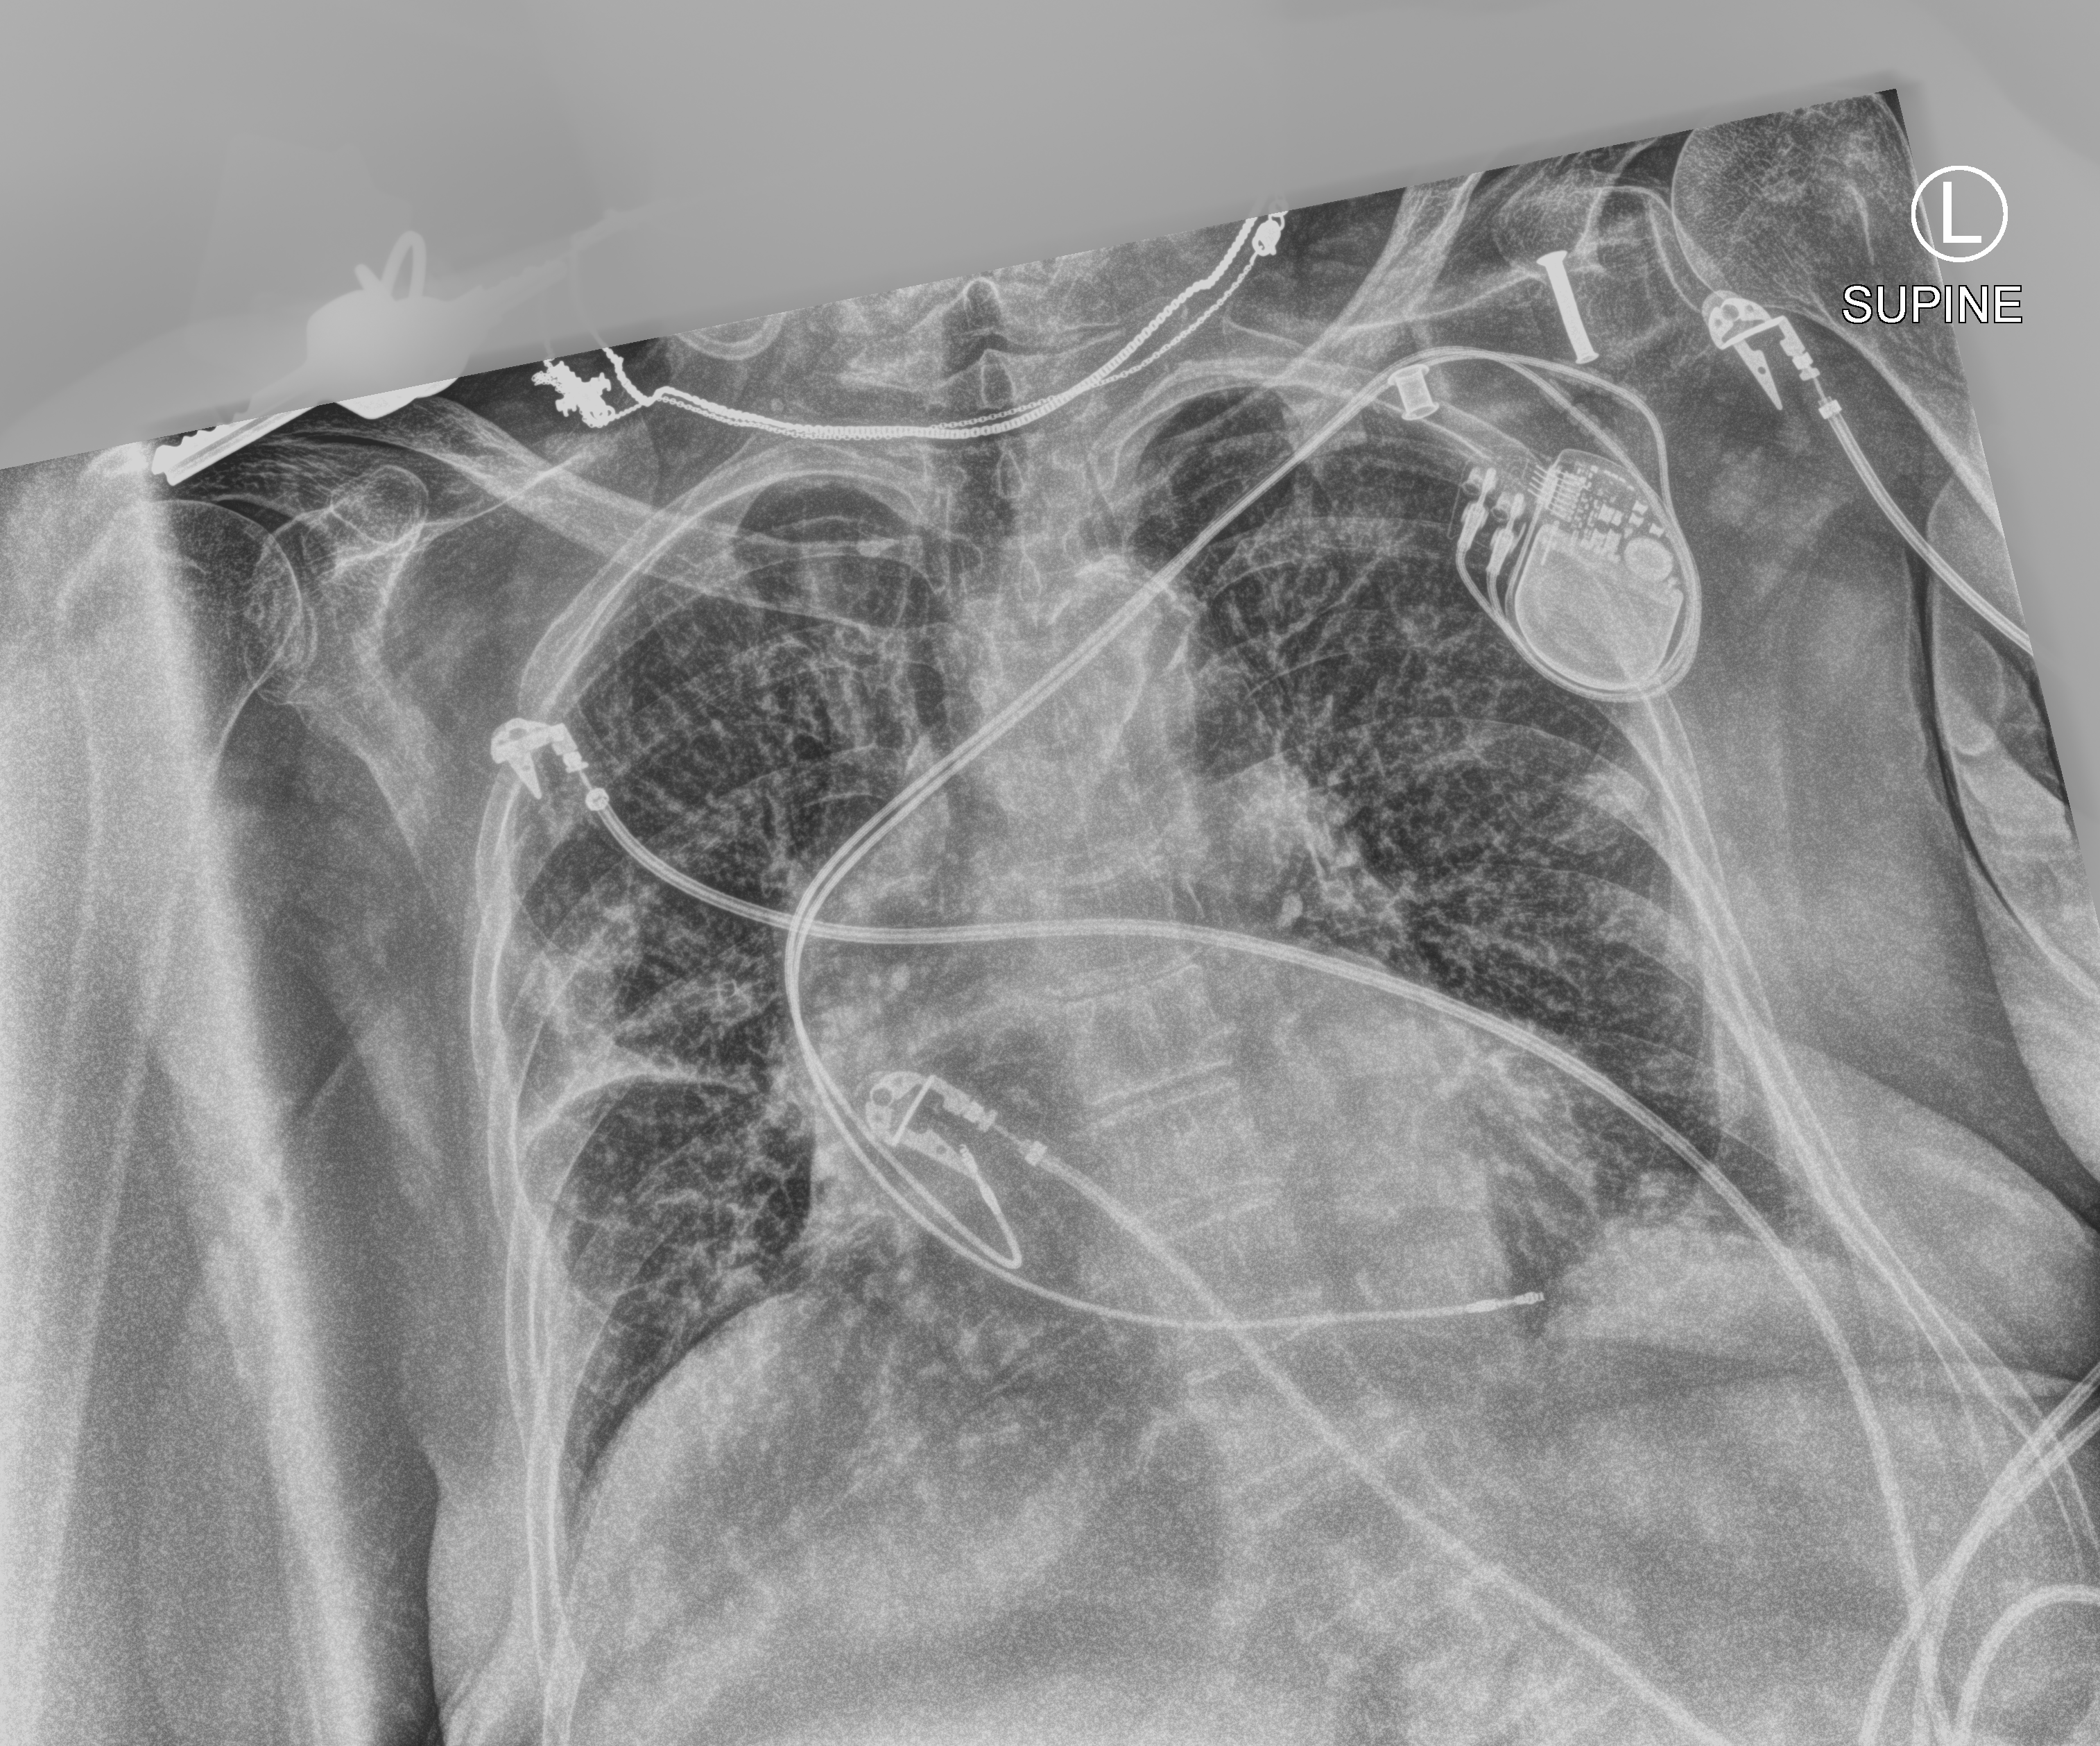
Chest X-ray (portable), anteroposterior (AP) projection. Patient hospitalised with COVID-19; female, aged 75–90 years.
Hospital-stay facts (about this admission, not read from this image; timing relative to this image not recorded): admitted to intensive care during this hospital stay: no; mechanically ventilated during this hospital stay: no.